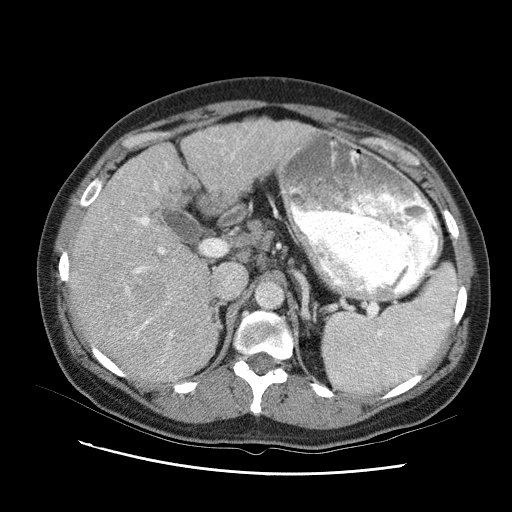
Contrast-enhanced abdominal CT (liver protocol), one axial slice; slice 59 of 95 in the series (ordered by position); reconstruction kernel STANDARD; 120 kVp; one of 2 acquisitions stored at this slice position; soft-tissue window (W 400 / L 40 HU); 2.5 mm slice thickness; 512 × 512 image matrix. From the clinical record (not read from this slice): diagnosis: hepatocellular carcinoma (patient treated with transarterial chemoembolisation; whether this scan precedes or follows treatment is not stated here); TNM stage (as recorded): Stage-I; Child-Pugh class: B; tumour differentiation: moderately differentiated; tumour nodularity: uninodular.
Structures marked on this image (semi-automatic segmentation, software-assisted and operator-edited):
- liver parenchyma outside the tumour (the mass and vessels are separate outlines, so this box may not span the whole liver): bounding box (x1, y1, x2, y2) in pixels: (68, 114, 320, 378)
- mass: (137, 286, 153, 305)
- liver vessels: (76, 129, 292, 345)